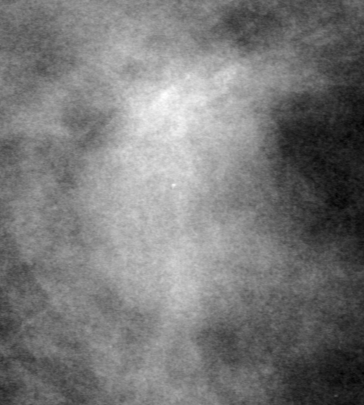
Cropped region of a digitized screen-film mammogram centred on a radiologist-marked abnormality, right breast, CC view.
Mass, shape oval, margins obscured; BI-RADS assessment category 0; subtlety rating 3 on a 1 (subtle) to 5 (obvious) scale; pathology (as recorded): benign.